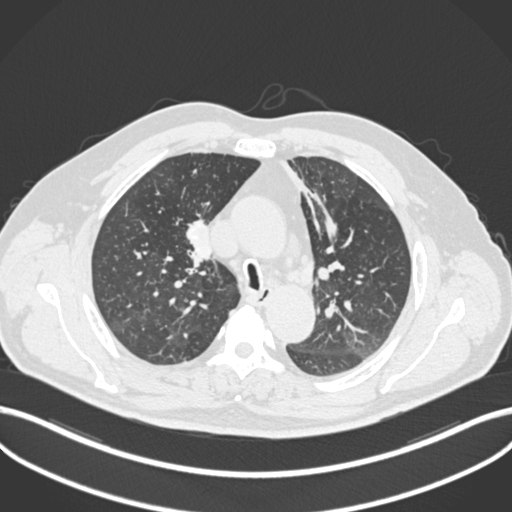
Chest CT, one axial slice; position 136 of 255 along the scan axis; reconstruction kernel B30f; lung window (W 1500 / L -600 HU); 512 × 512 image matrix, field of view 400 × 400 mm. Male patient, age 60 years. From the clinical record (not read from this slice): clinical TNM (as recorded): T1b N1 M0.
Structures marked on this image (bounding box drawn by a radiologist):
- lung tumour (recorded histology: squamous cell carcinoma): bounding box [x1, y1, x2, y2] px = [184, 216, 221, 270]